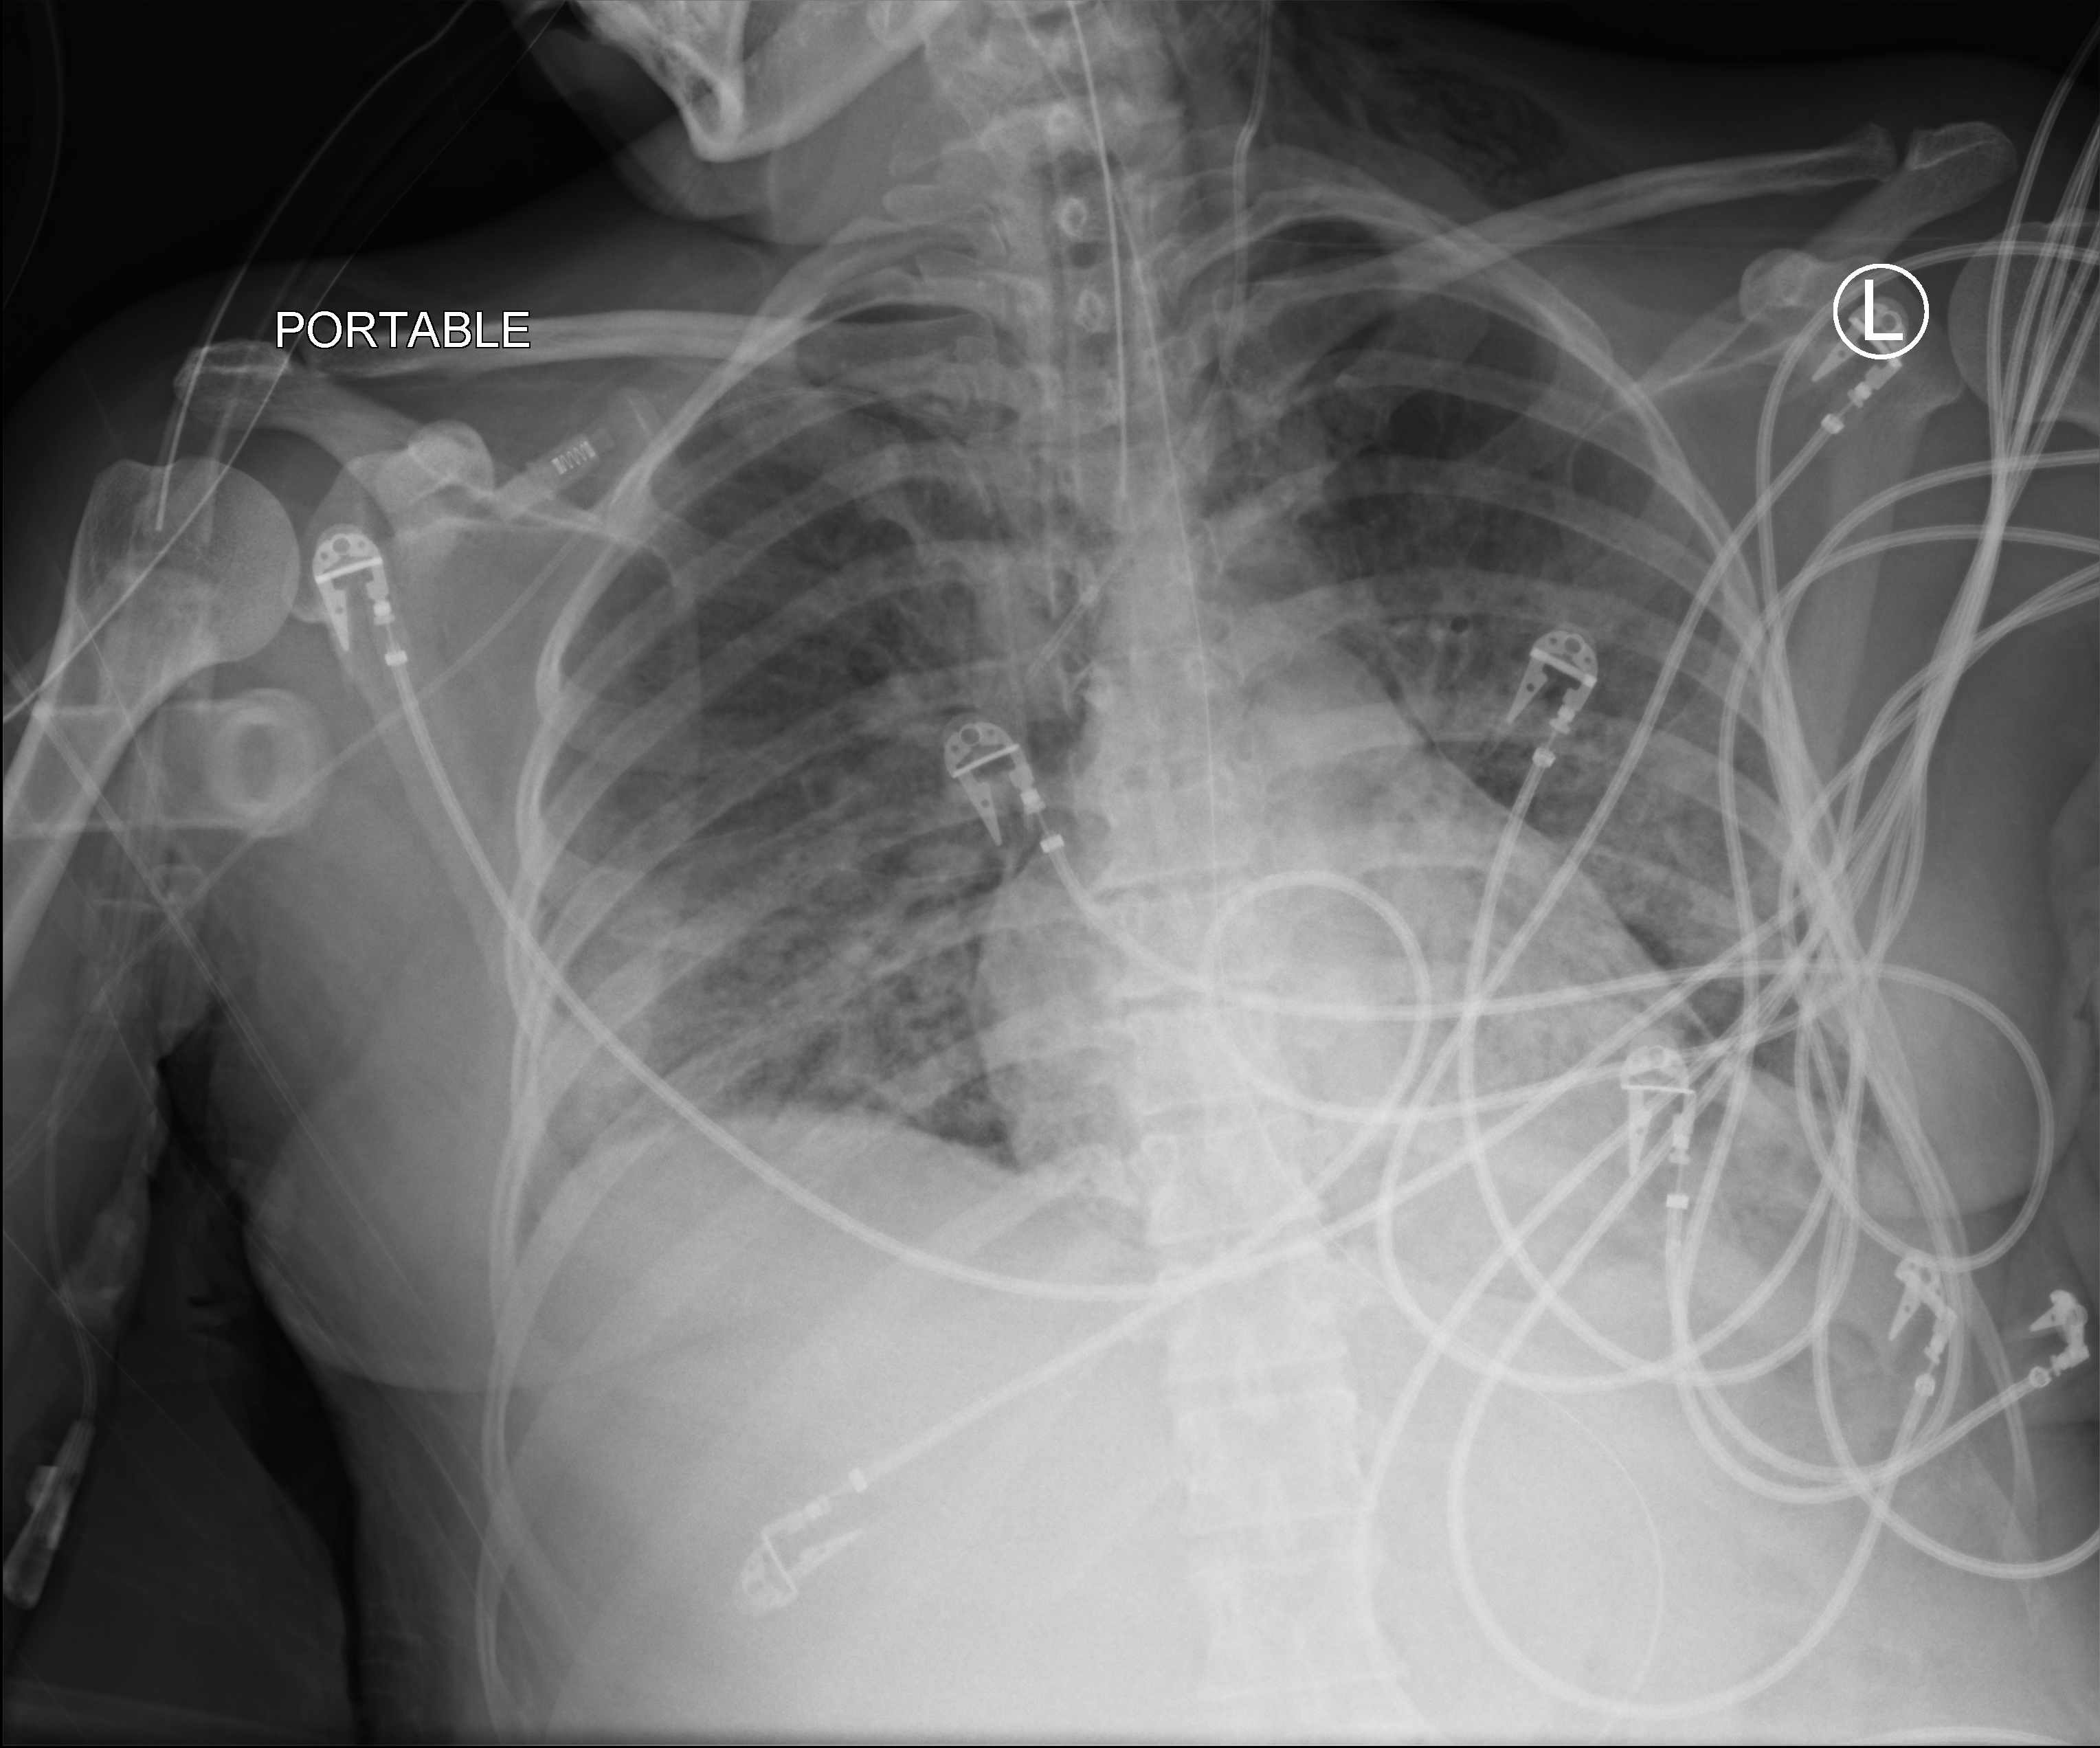
Bedside chest radiograph (computed radiography), anteroposterior (AP) projection. Patient hospitalised with COVID-19; female, aged 18–59 years.
Admission-level facts for this patient (not findings on this image; timing relative to this image not recorded): COPD (admission record): no; mechanically ventilated during this hospital stay: yes; hypertension (admission record): no.